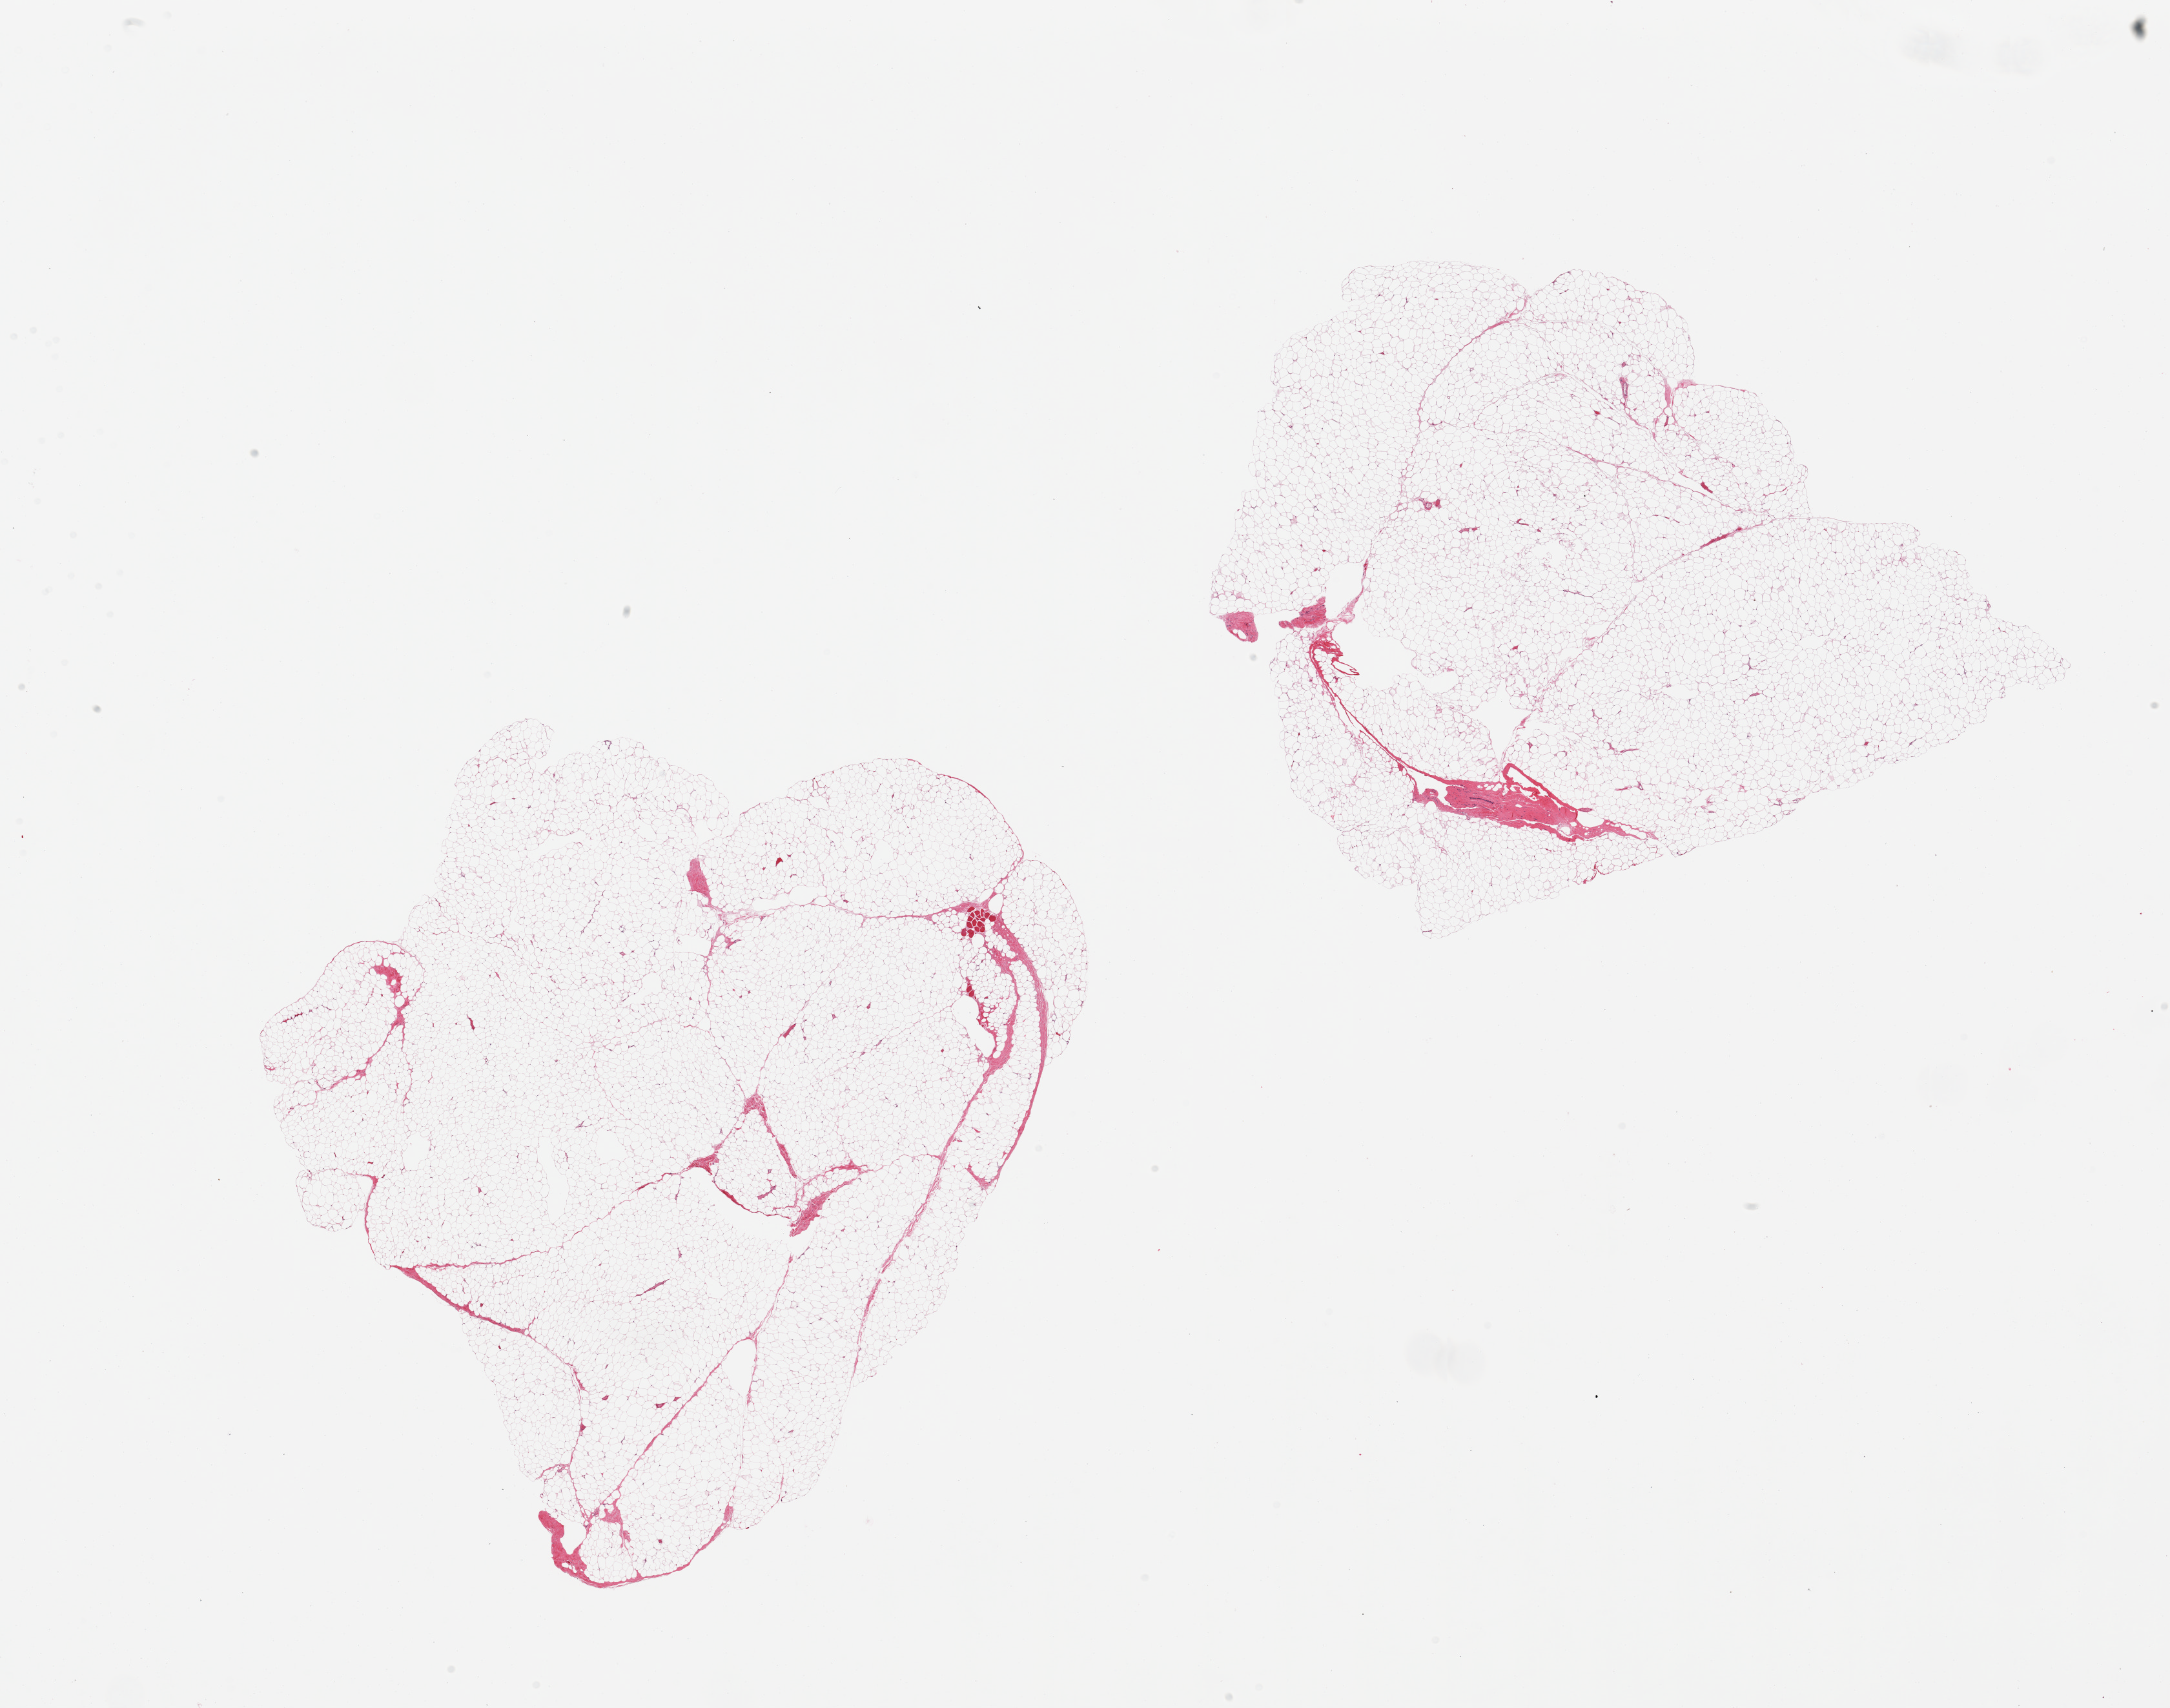
Haematoxylin and eosin whole-slide image, brightfield, low-resolution overview of the scanned area, about 26.6 x 20.9 mm (slide scanned at 20x); PAXgene-fixed, paraffin-embedded tissue; target tissue: breast; donor tissue sample. Male donor.
Review note (as recorded): 2 pieces; fatty tissue without ducts or fibrous stroma.